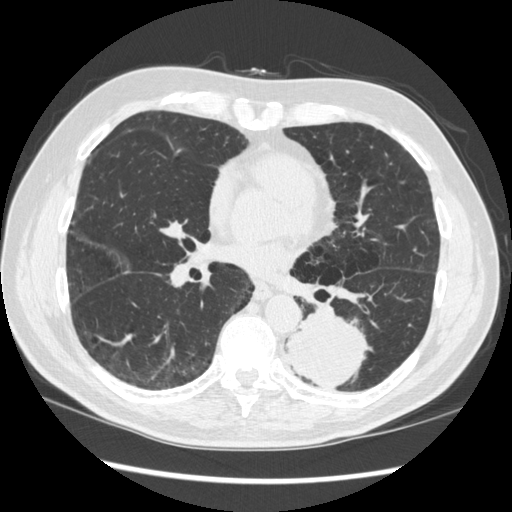
Low-dose screening chest CT, axial slice; baseline screening round; lung window (W 1500 / L -600 HU); 512 × 512 image matrix, field of view 360 × 360 mm. Male participant, aged 72 years at enrolment.
Expert-annotated lung lesion, box from (x=267, y=303) to (x=371, y=395) px. The screening reader recorded 2 non-calcified nodules or masses ≥4 mm on this exam; which of them this box marks is not recorded. Official screen result: positive, change unspecified: nodule(s) >= 4 mm or enlarging nodule(s), mass(es), or other non-specific abnormalities suspicious for lung cancer.